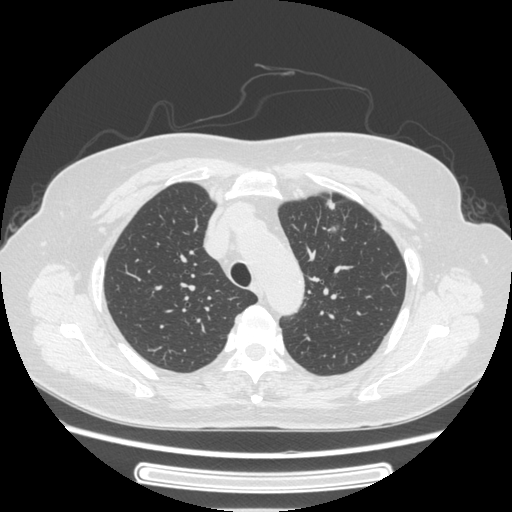
Chest CT, one axial slice; position 180 of 227 along the scan axis; reconstruction kernel STANDARD; 120 kVp; lung window (W 1500 / L -600 HU); 1.25 mm slice thickness; 512 × 512 image matrix, field of view 363 × 363 mm. Female patient, age 77 years. Case-level facts recorded for this patient, not image findings: clinical TNM (as recorded): T1c N3 M0.
Structures marked on this image (rectangle marked by the reading radiologist):
- lung tumour (recorded histology: adenocarcinoma): box from (x=319, y=195) to (x=338, y=212) px